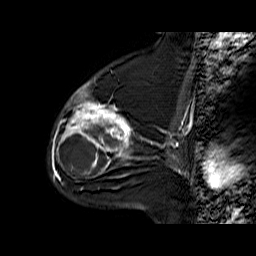
Breast MRI (dynamic contrast-enhanced), one sagittal slice. Position 40 of 60 along the scan axis. Dynamic contrast-enhanced series, time point 2 of 6 at this slice position (early post-contrast). 1.5 T. TE 6.3 ms, TR 32.9 ms. 4 mm slice thickness. 256 × 256 image matrix, field of view 200 × 200 mm. Female patient. From the clinical record (not read from this slice): setting: breast cancer imaged before/during neoadjuvant chemotherapy; receptor status: triple-negative.
Structures marked on this image (semi-automatically segmented with operator editing):
- analysis volume of interest (the breast-tissue region the enhancement analysis was run in; not a lesion): bounding box [x1, y1, x2, y2] px = [56, 76, 140, 170]
- tumour enhancement mask (voxels above the 100 % enhancement threshold inside the analysis volume of interest): [59, 83, 131, 170]